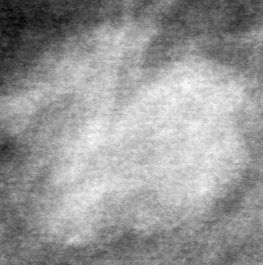
Crop from a digitized film mammogram around one marked abnormality, left breast, MLO view, BI-RADS breast density category 2 (scale 1–4).
Finding: mass, shape lobulated, margins circumscribed; BI-RADS assessment category 4; pathology result (as recorded, not read from the image): benign.